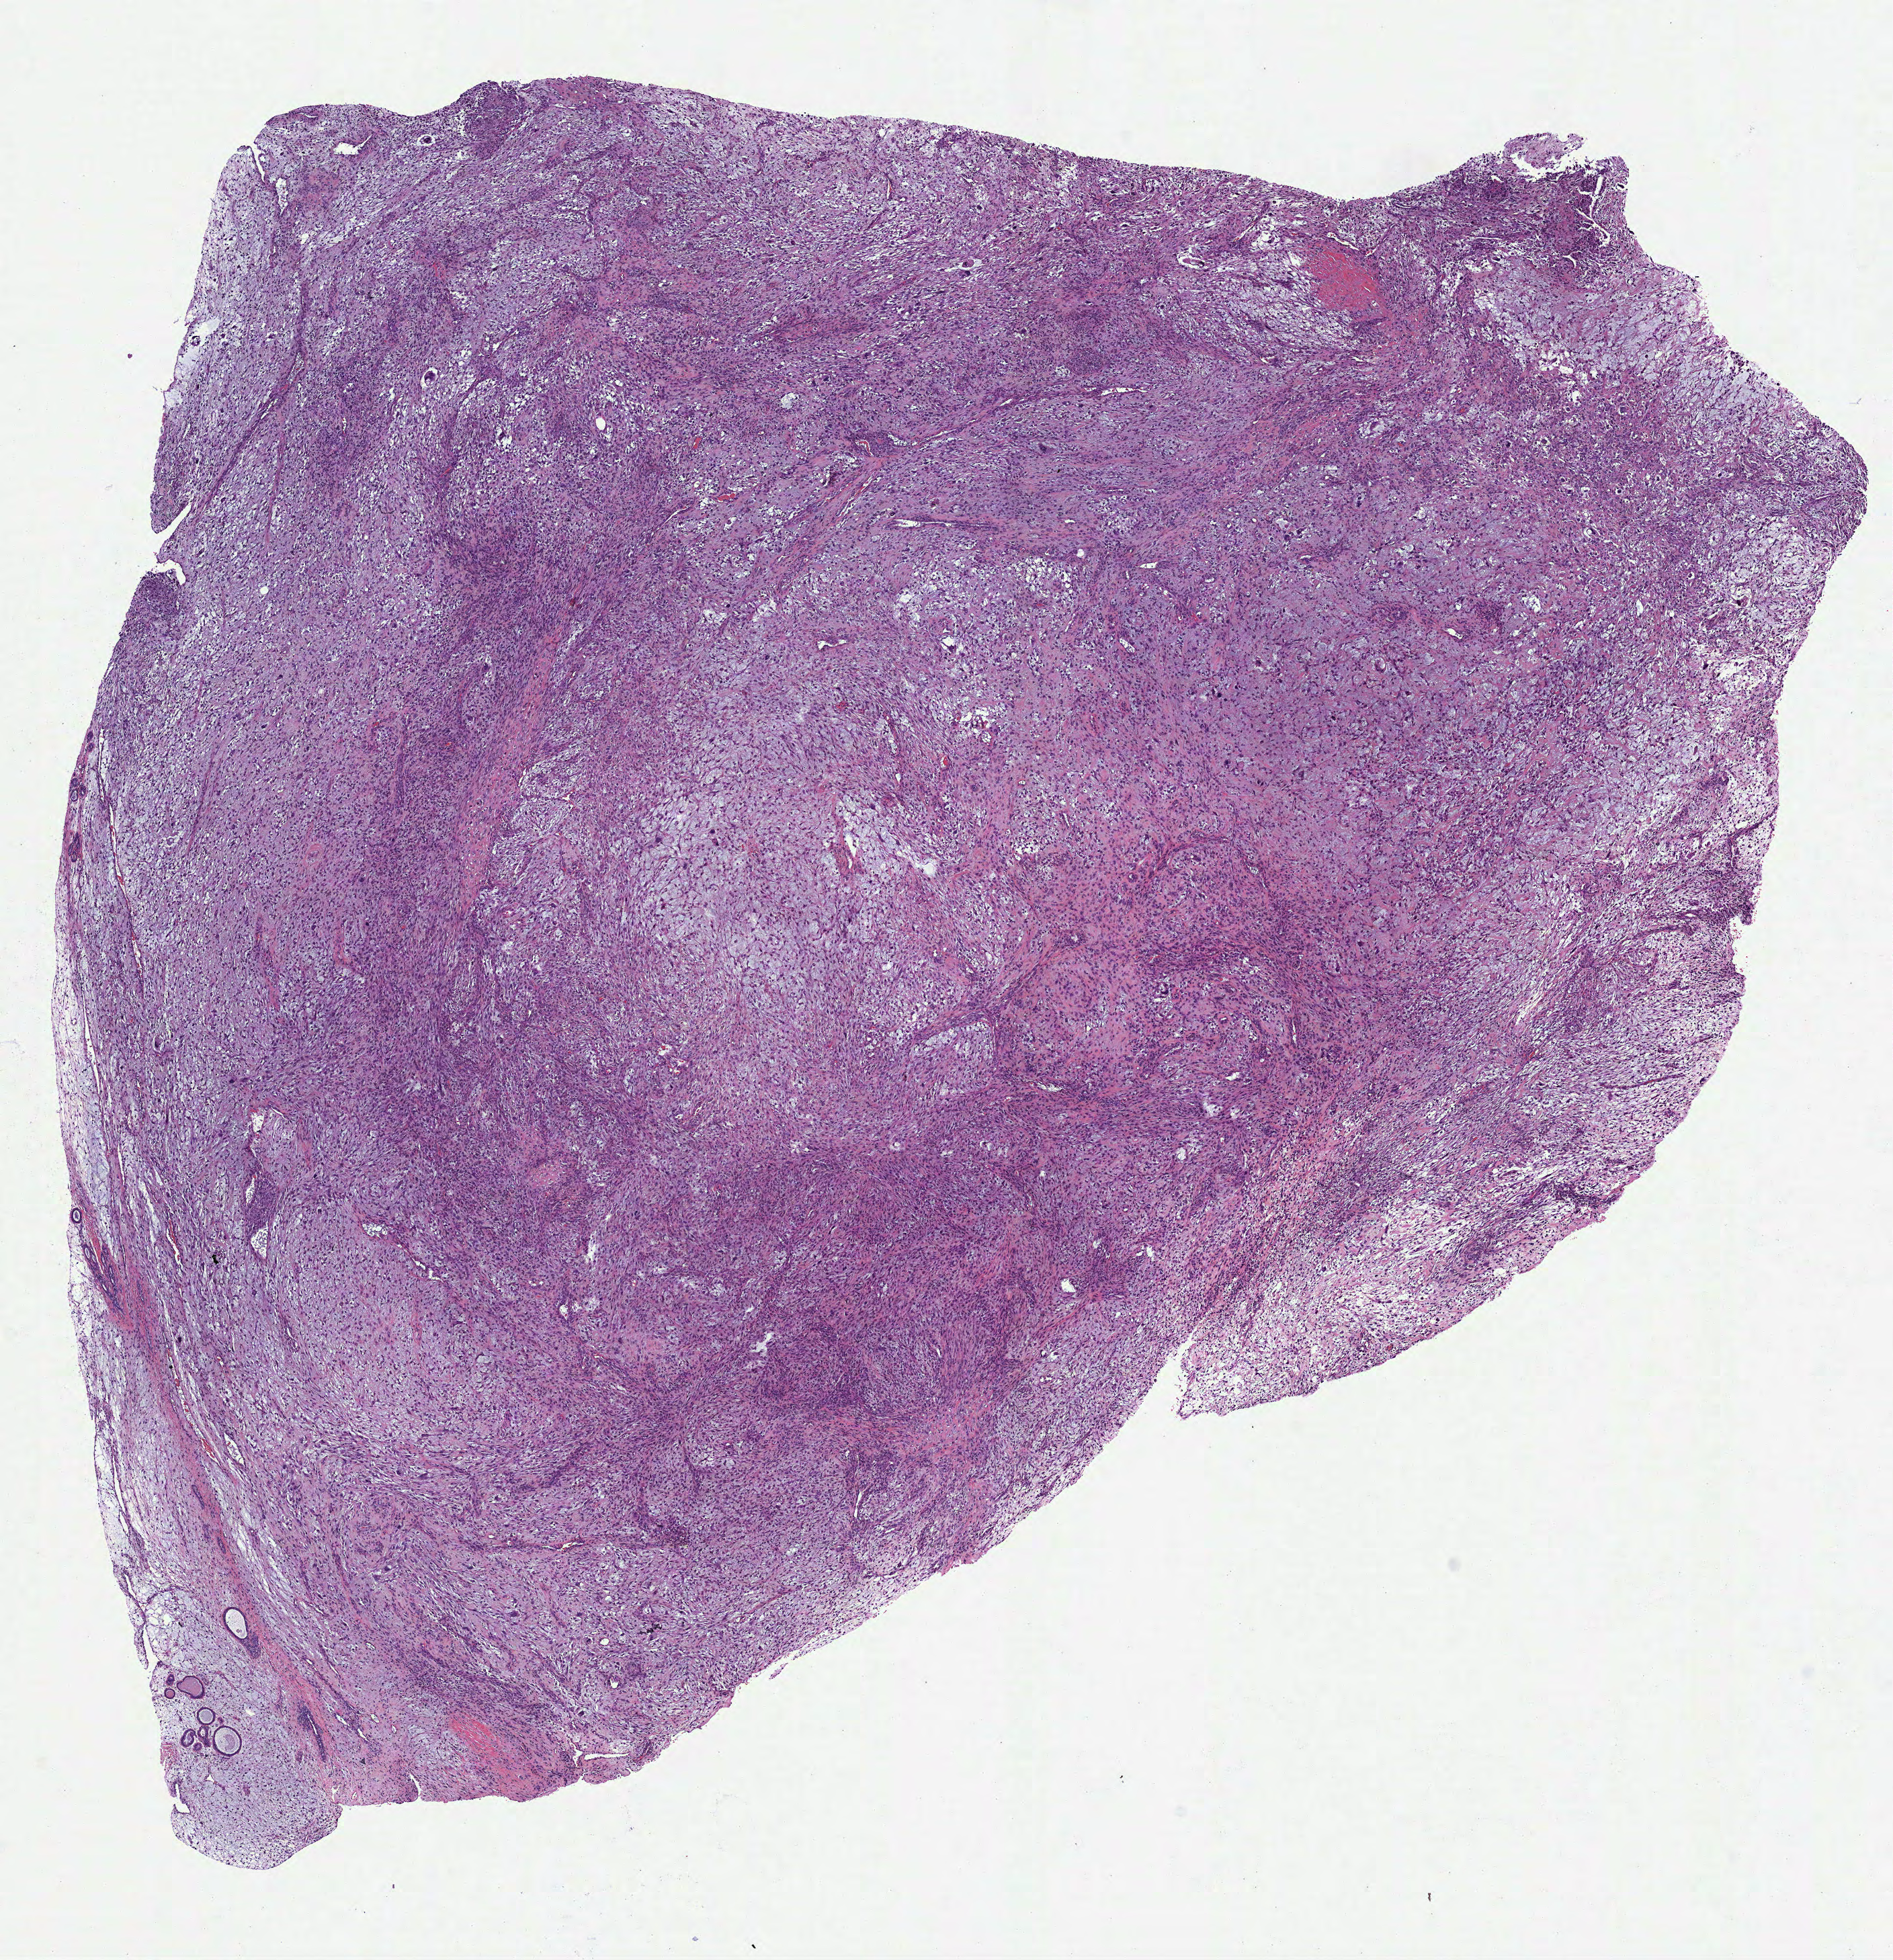
Whole-slide histology image, H&E-stained, low-resolution overview of the scanned area, about 11.4 x 11.8 mm, formalin-fixed paraffin-embedded (FFPE) diagnostic section, sample: primary tumour, breast. Patient: female, age at initial diagnosis 56 years.
Pathologic diagnosis: Metaplastic carcinoma, NOS. Lymph nodes positive (case pathology): 0 of 1 examined. AJCC pathologic stage: IIB (7th edition).